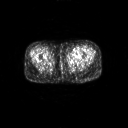
FDG PET of an extremity soft-tissue mass (from a PET/CT study), one axial slice. Position 9 of 267 along the scan axis. 128 × 128 image matrix, field of view 700 × 700 mm. Female patient, age 47 years. Case-level facts recorded for this patient, not image findings: histological type: myxofibrosarcoma; grade: intermediate; site of the primary tumour: left thigh.
Annotated regions visible in this slice (expert contour drawn on MRI and transferred to this co-registered scan by the dataset authors):
- gross tumour volume including surrounding oedema: bounding box [x1, y1, x2, y2] px = [68, 53, 81, 61]